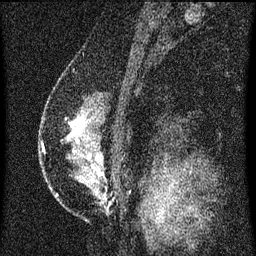
Breast MRI (dynamic contrast-enhanced), one sagittal slice; position 39 of 60 along the scan axis; dynamic contrast-enhanced series, image 2 of 3 at this slice position (ordered by acquisition); 1.5 T; TE 4.2 ms, TR 8 ms; 2 mm slice thickness; 256 × 256 image matrix, field of view 180 × 180 mm. Female patient, age 47 years.
Annotated regions visible in this slice (semi-automatically segmented with operator editing):
- analysis volume of interest (the breast-tissue region the enhancement analysis was run in; not a lesion): bounding box (x1, y1, x2, y2) in pixels: (51, 96, 120, 203)
- tumour enhancement mask (voxels above the 70 % enhancement threshold inside the analysis volume of interest): (71, 118, 85, 135)